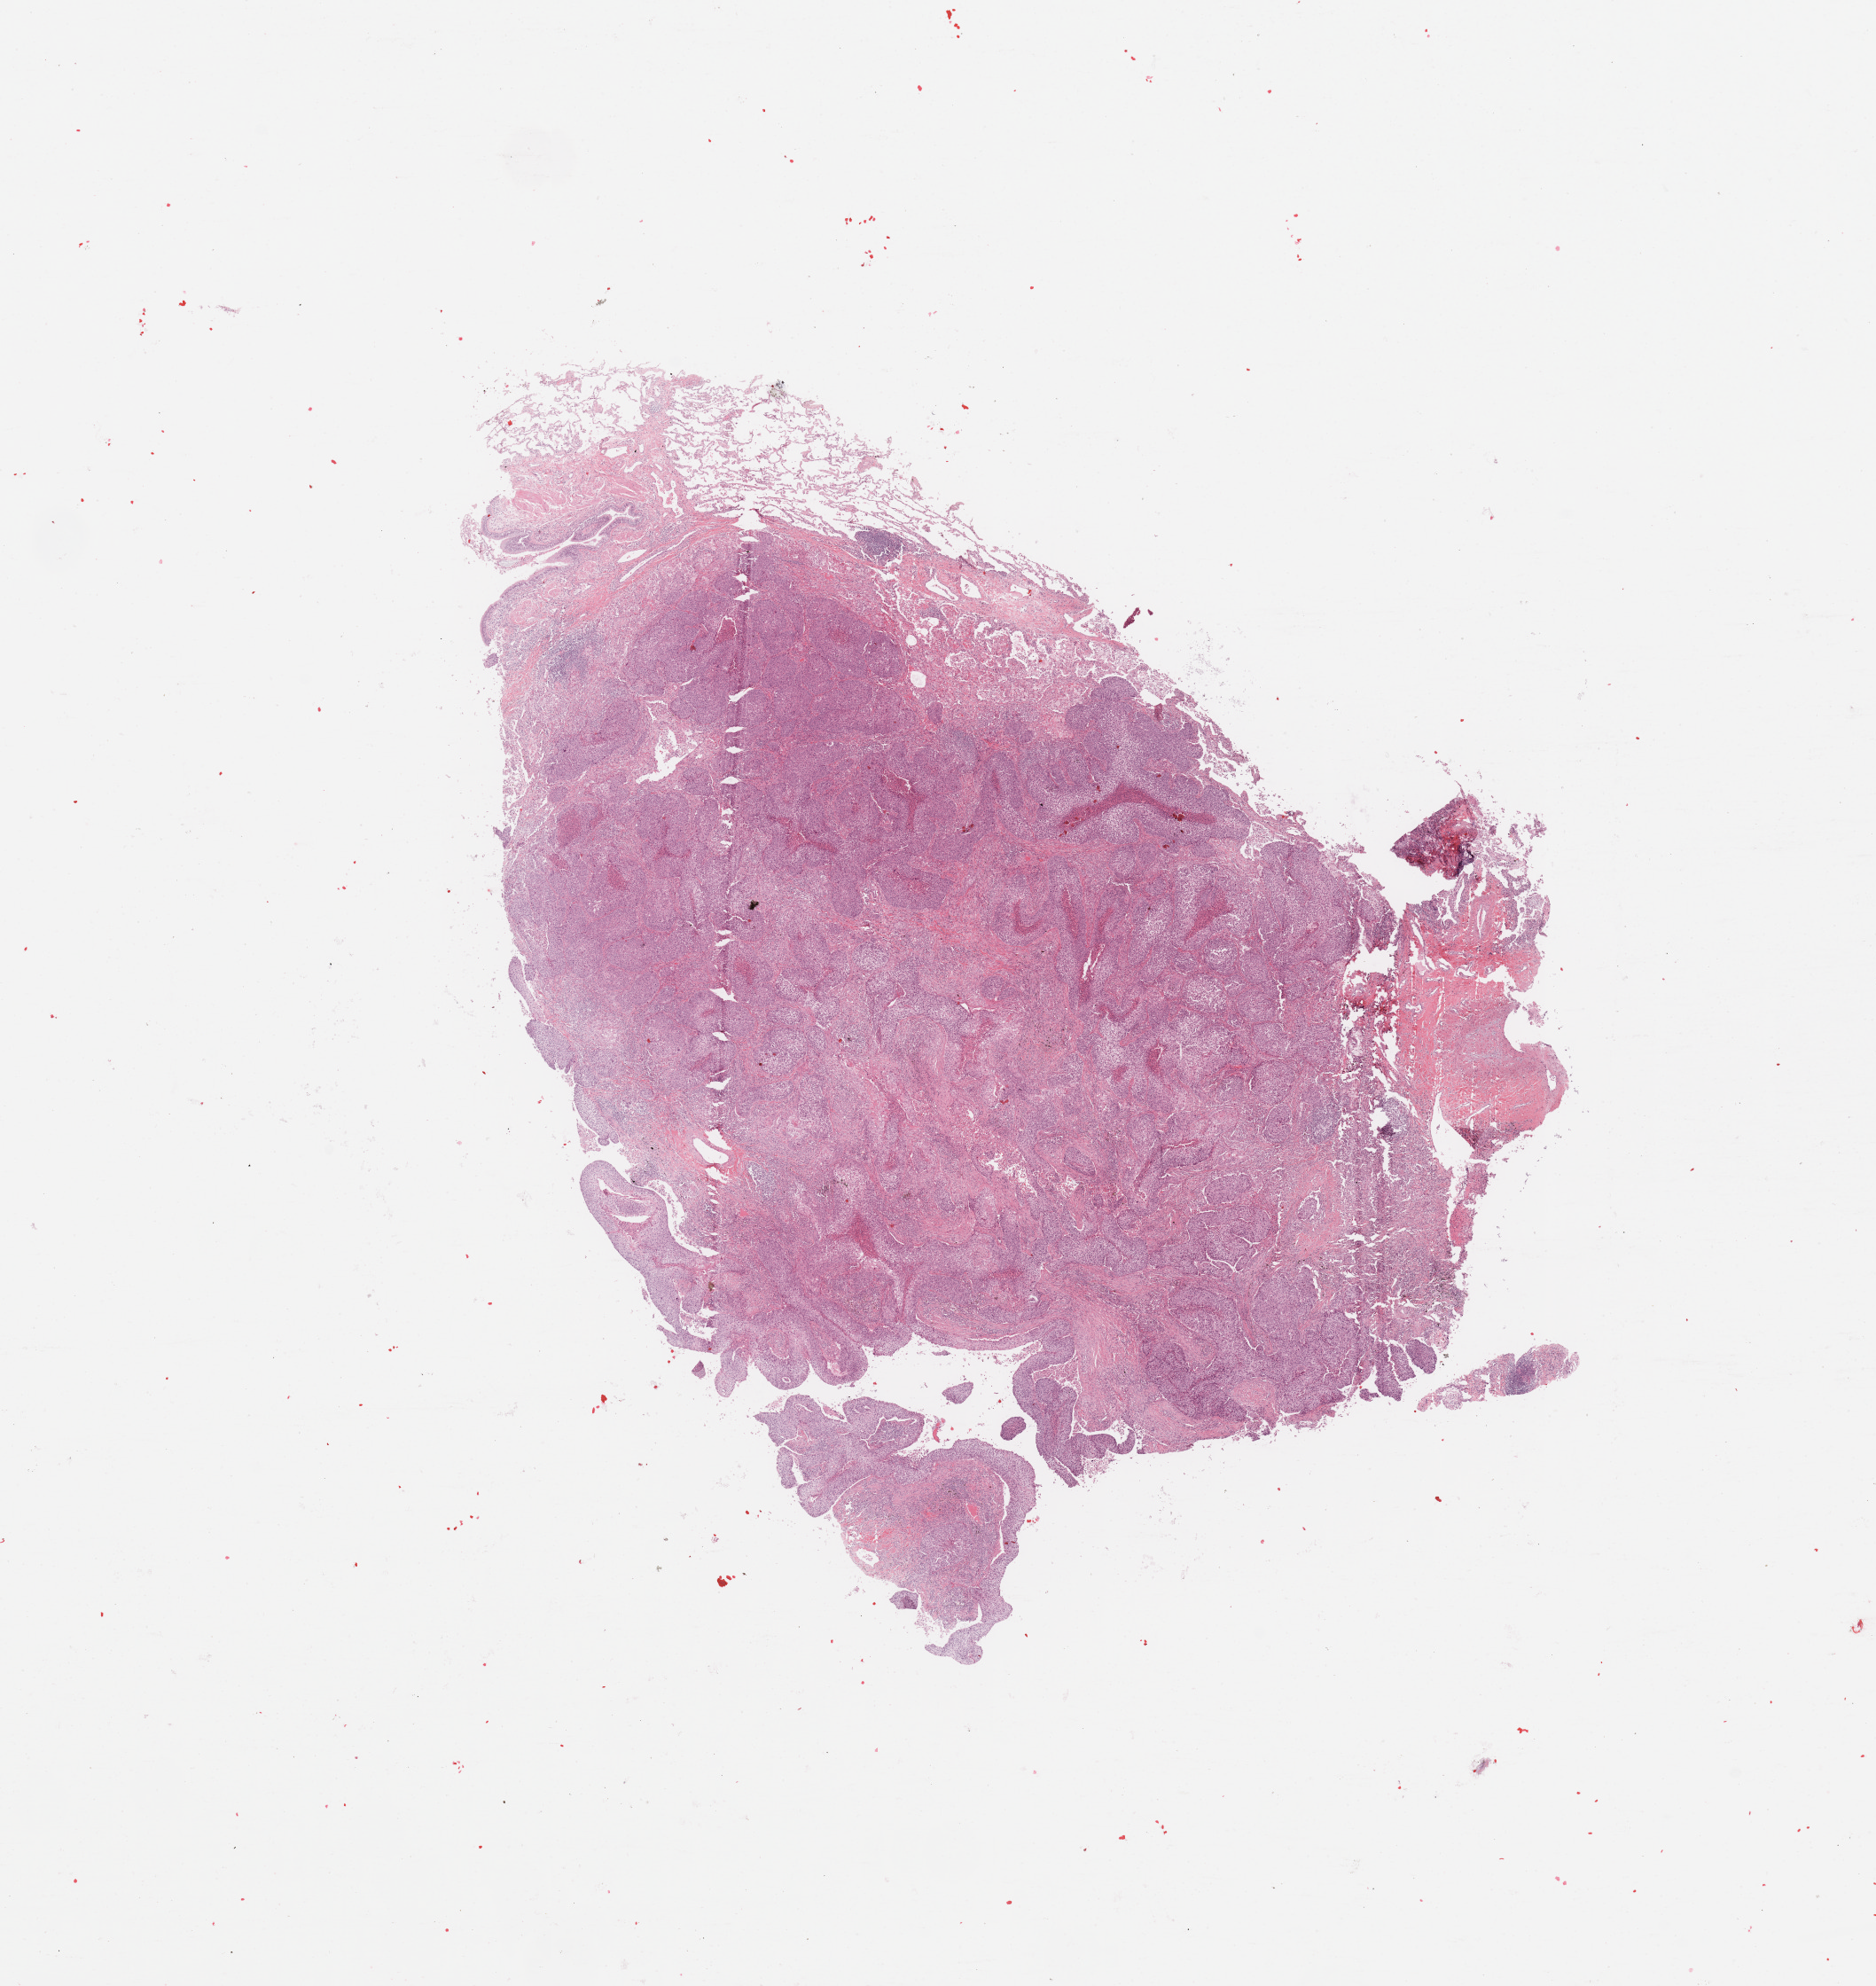
H&E whole-slide image — a low-resolution overview of the entire scanned area, about 16.7 x 17.7 mm; tumour tissue sample, sampled site: lung. Patient: male, age 68 years. Histologic grade: G3 (poorly differentiated). Composition of this section per pathologist review: tumour nuclei 80%, necrosis 10%.
* primary tumour site (as recorded): right upper lobe
* histologic diagnosis: Squamous cell carcinoma, NOS
* AJCC pathologic stage: IB